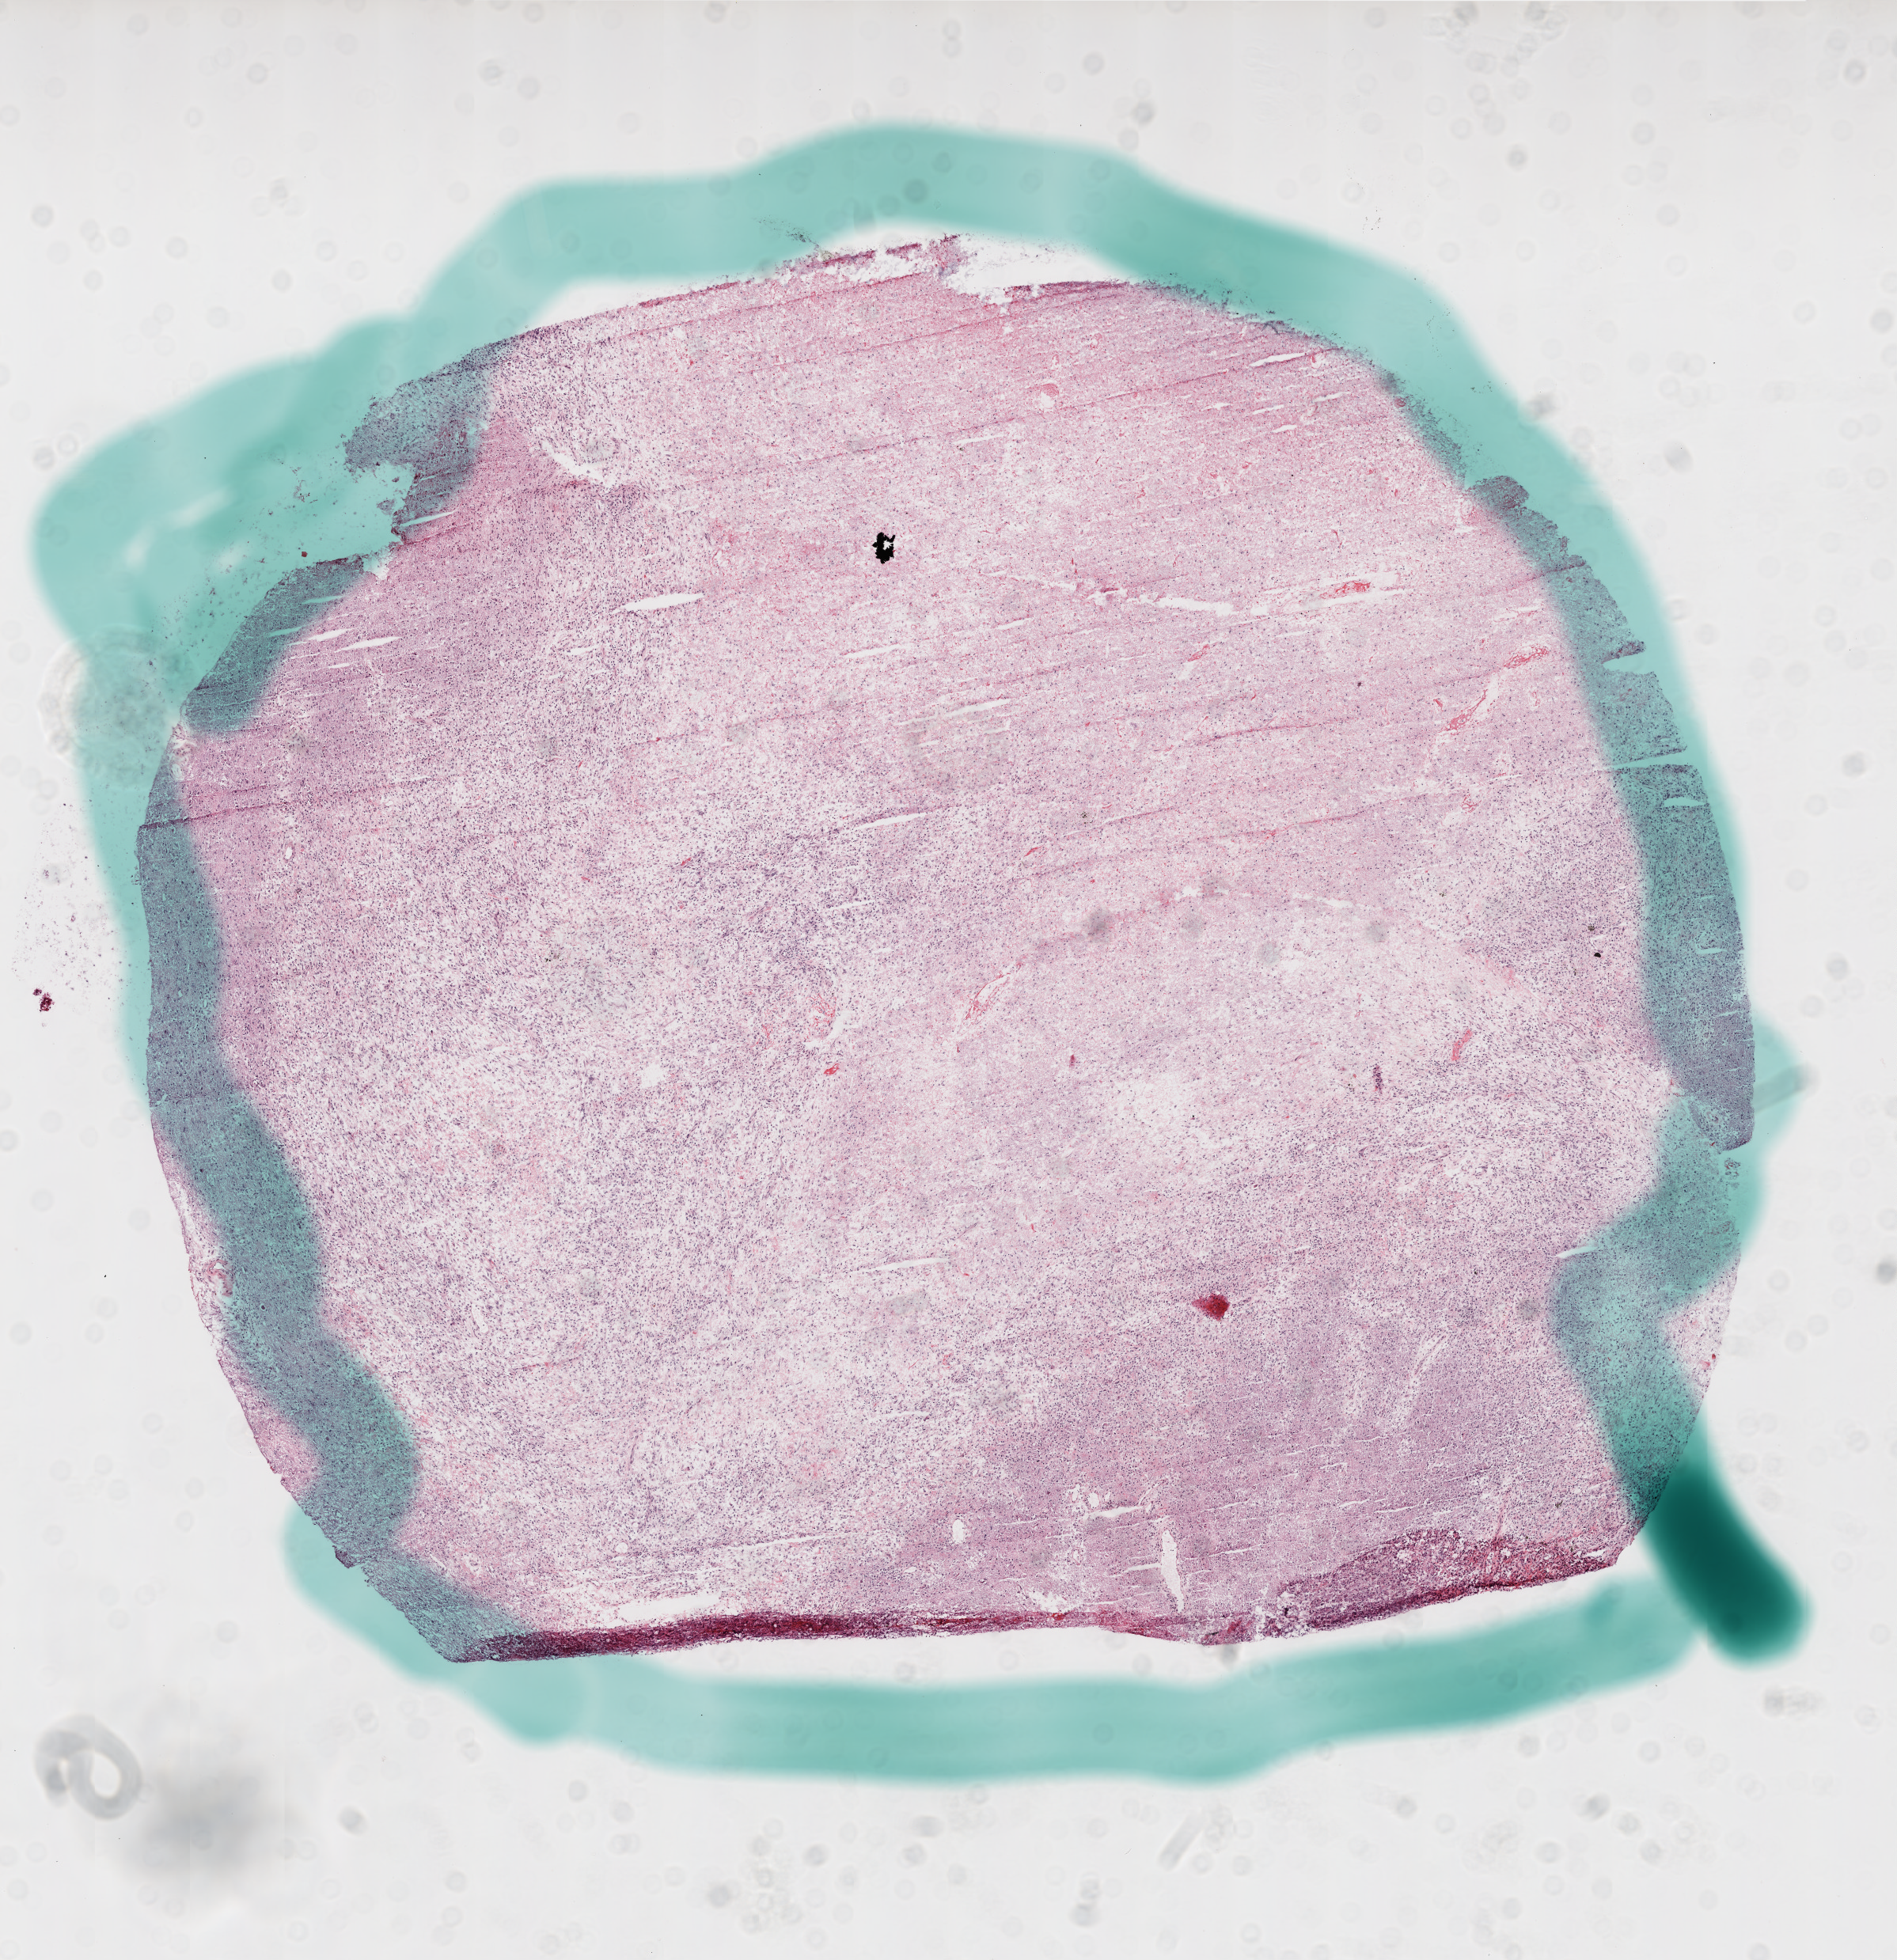
H&E whole-slide image, whole scanned area (about 9.6 x 10.0 mm, slide scanned at 20x) shown as a low-resolution overview. Frozen section from the bottom of the tissue portion. Primary tumour sample from the brain. Male patient; age at initial diagnosis 40 years. Composition of this section per pathologist review: tumour cells 50%, tumour nuclei 95%, normal cells 0%, stromal cells 50%, necrosis 0%. Infiltration values recorded for this section: lymphocyte infiltration 0%, monocyte infiltration 0%, neutrophil infiltration 0%.
Diagnosis: Glioblastoma.